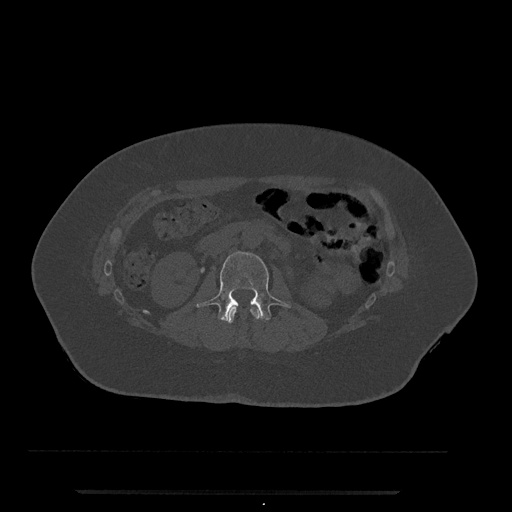
CT including the spine, one axial slice; position 48 of 797 along the scan axis; reconstruction kernel Br40s/3; 120 kVp; bone window (W 1800 / L 400 HU); 512 × 512 image matrix. Patient: female, 51 years. From the clinical record (not read from this slice): primary cancer: neuro; vertebrae with lytic lesions (as recorded): T8.
Annotated regions visible in this slice (semi-automatic segmentation, software-assisted and operator-edited):
- L1 vertebra: bounding box [x1, y1, x2, y2] px = [227, 306, 261, 324]
- L2 vertebra: [196, 251, 291, 322]